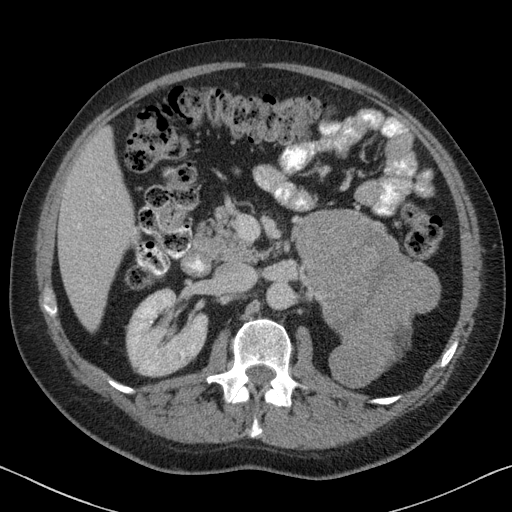
Contrast-enhanced abdominal CT, one axial slice. Reconstruction kernel B31f. 120 kVp. Intravenous contrast given. Soft-tissue window (W 400 / L 40 HU). 512 × 512 image matrix, field of view 366 × 366 mm. Patient: male, 51 years. From the clinical record (not read from this slice): diagnosis: adrenocortical carcinoma; tumour side: left adrenal.
Structures marked on this image (semi-automatically segmented with operator editing):
- mass: box from (x=292, y=210) to (x=439, y=387) px